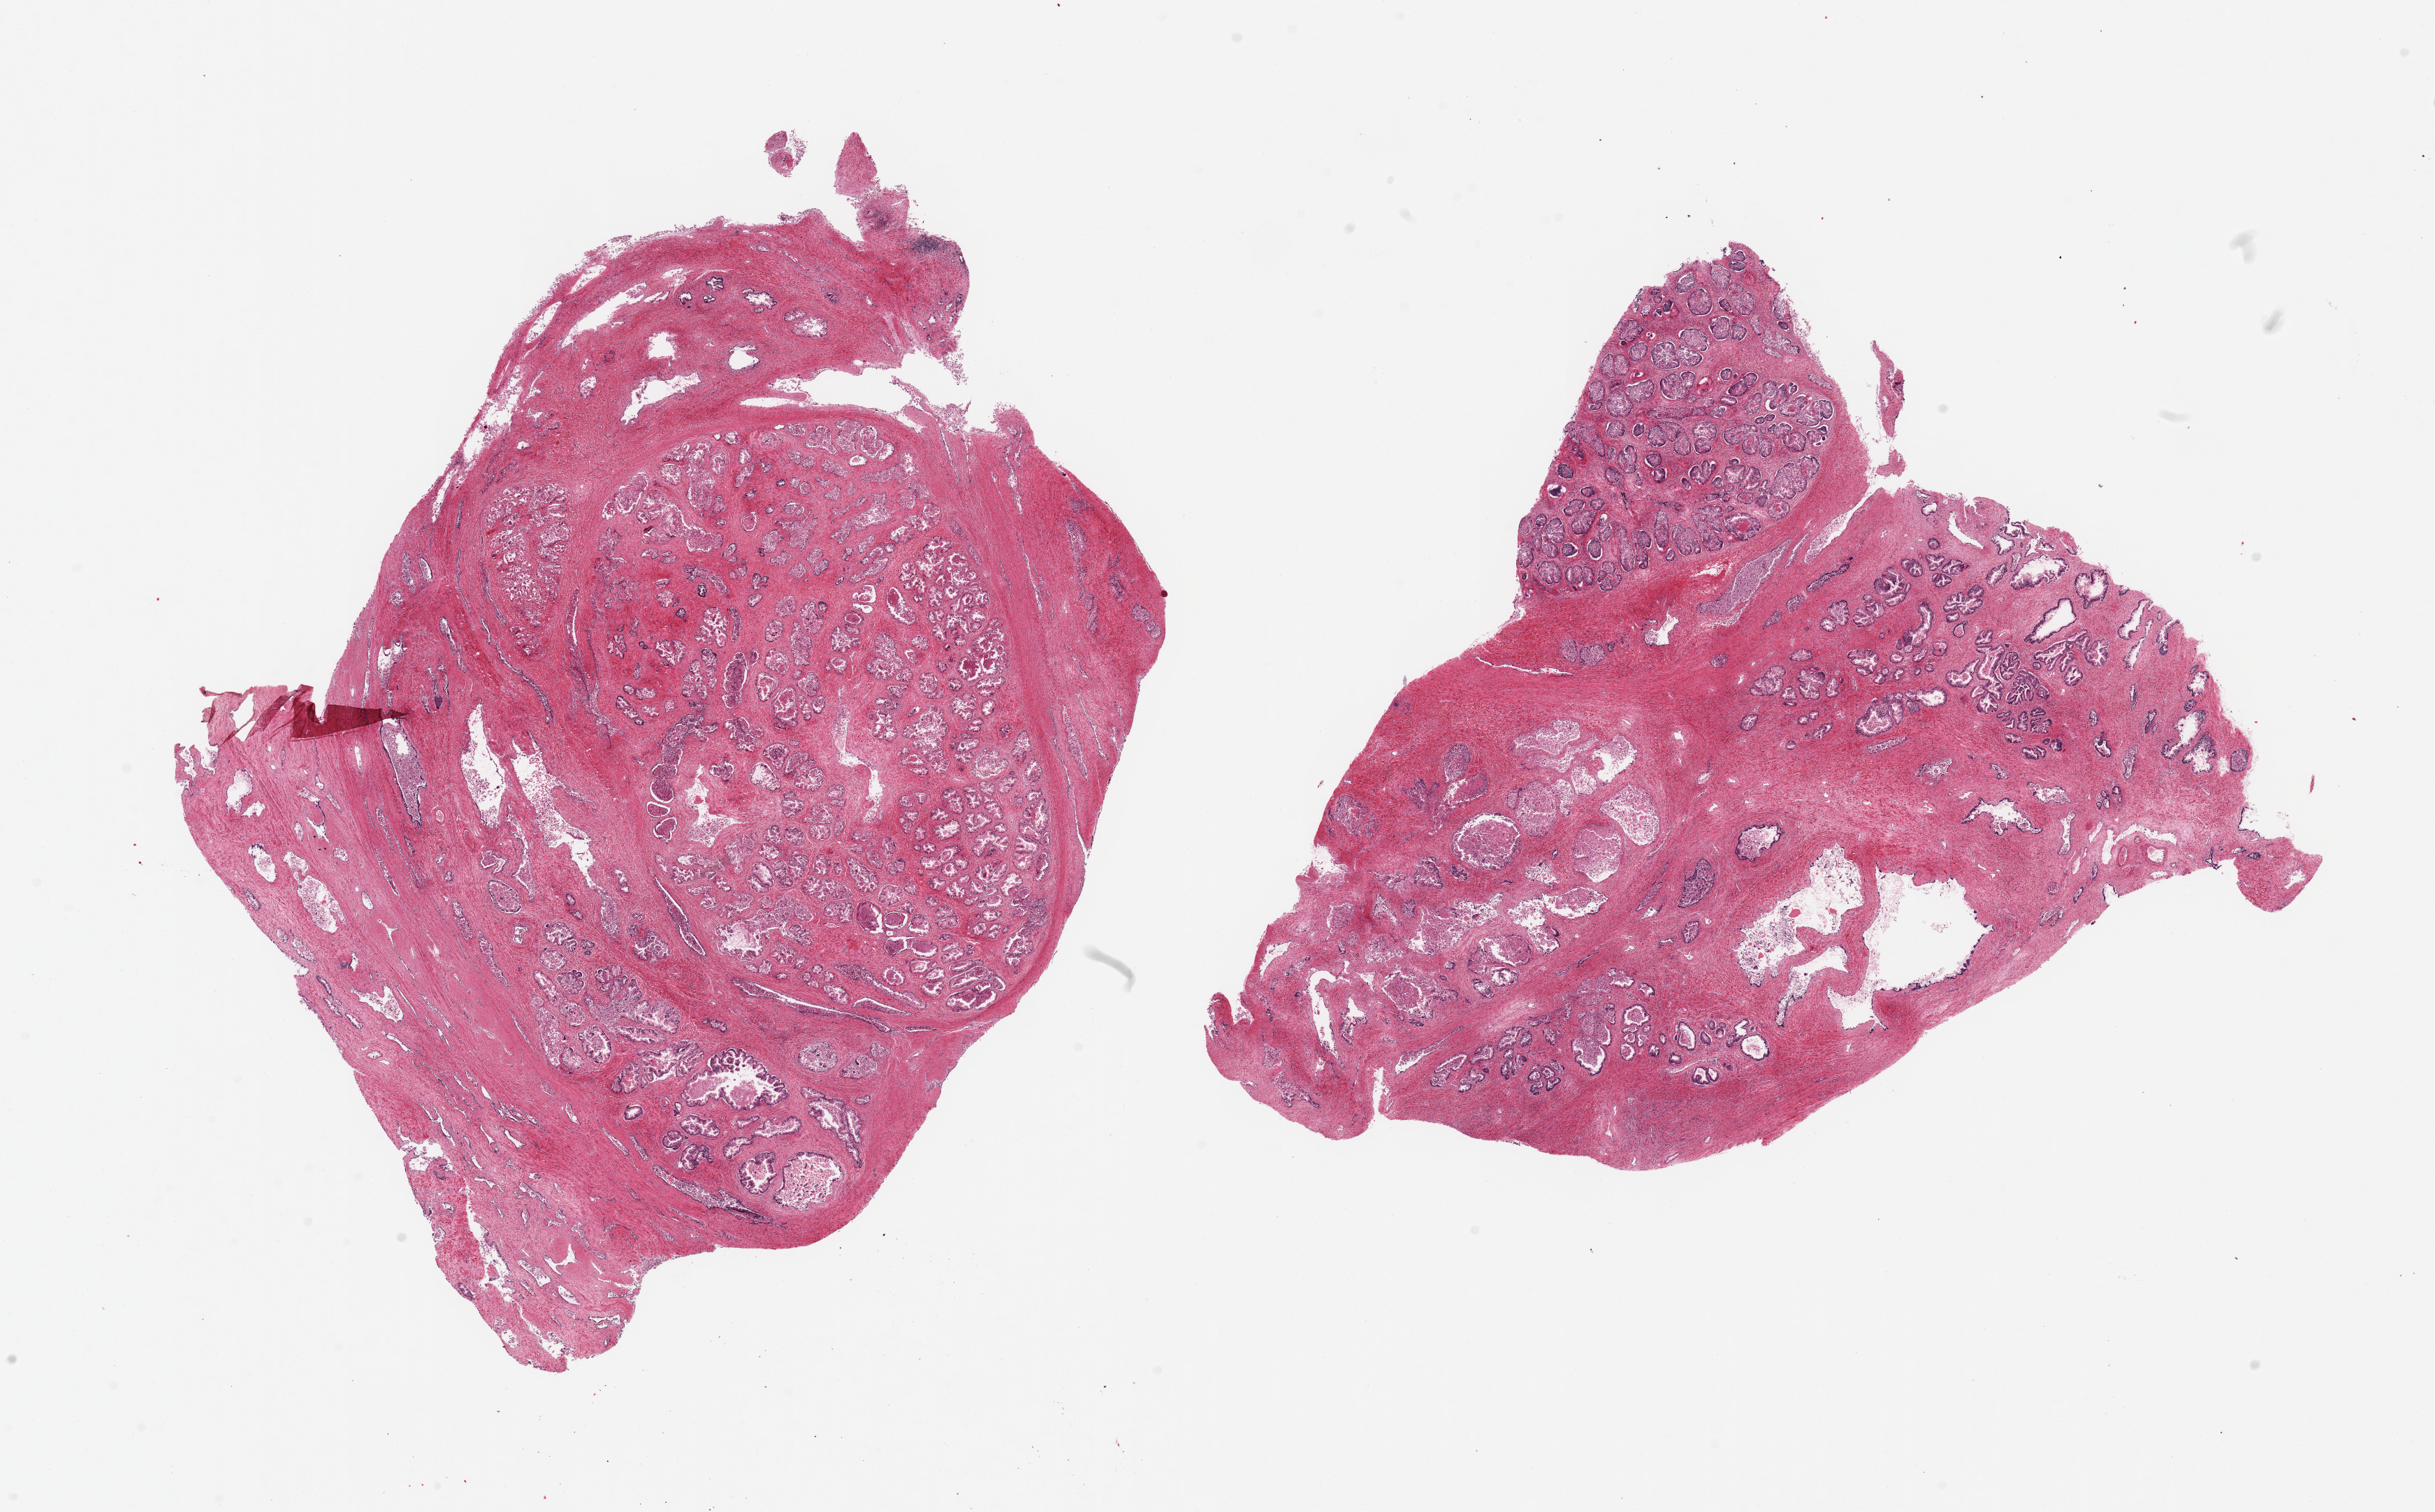
Digitized H&E-stained section, brightfield, low-resolution overview of the scanned area, about 27.6 x 17.1 mm. PAXgene-fixed paraffin-embedded (PFPE) section. Sampled site (target tissue): prostate. Tissue donor sample. Donor sex: male.
Reviewer comment on this tissue sample: 2 pieces; nodular hyperplasia.